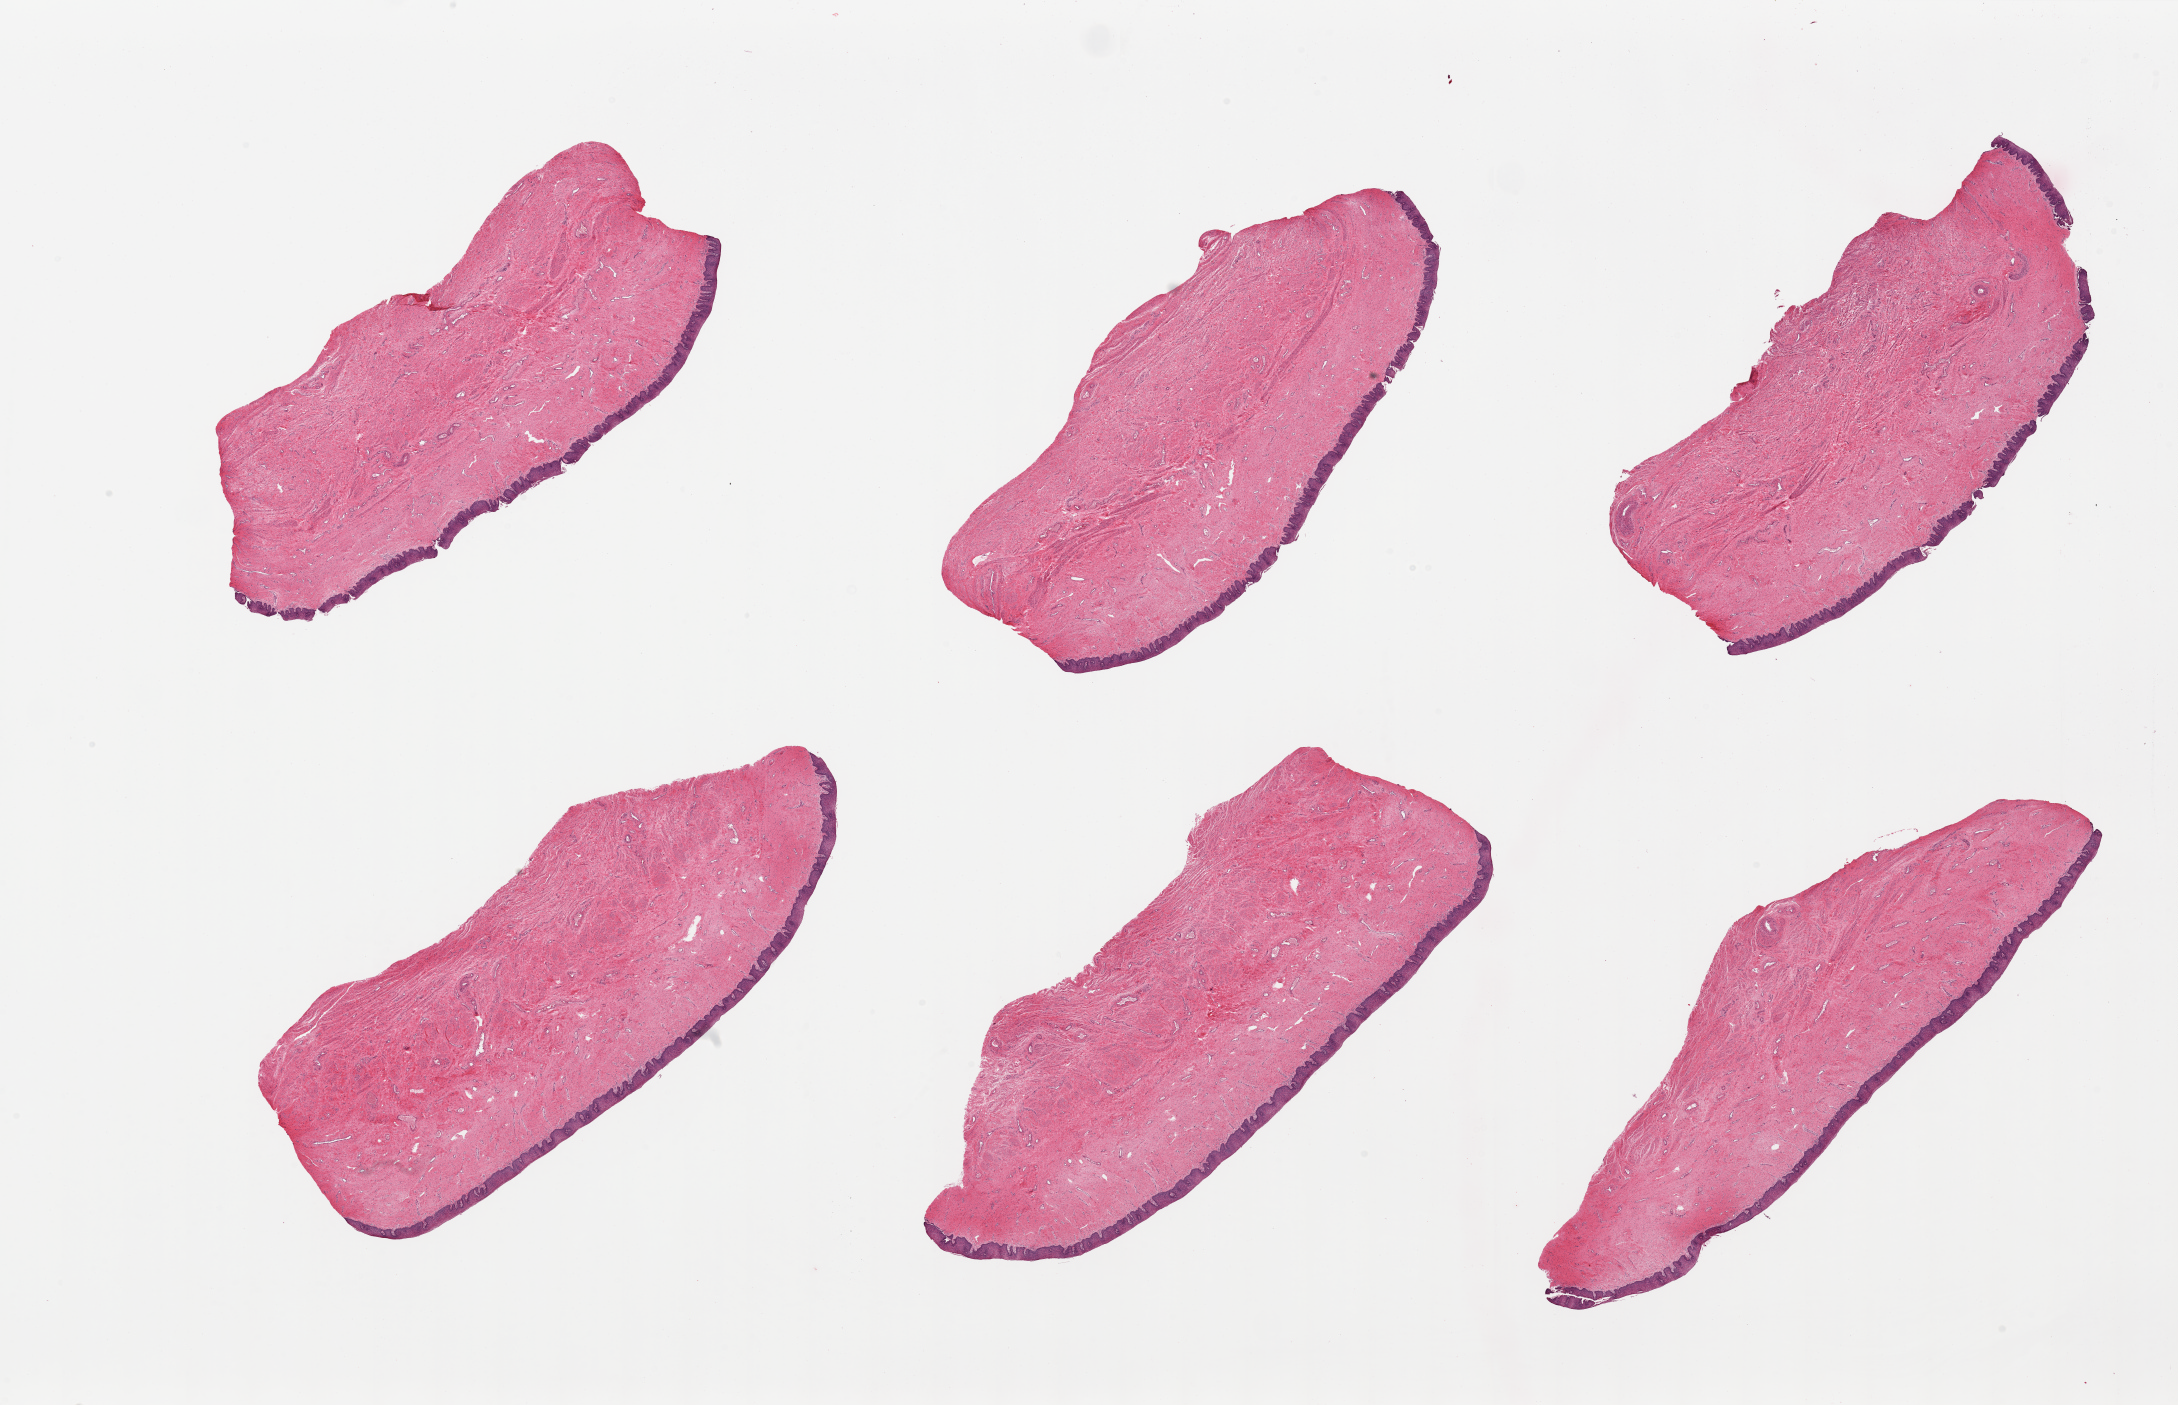
Whole-slide image, H&E stain, whole scanned area (about 34.5 x 22.2 mm, from a 20x scan) shown as a low-resolution overview; PAXgene-fixed, paraffin-embedded tissue; section of vagina (target tissue); donor tissue sample. Donor: female.
Review note (as recorded): 6 pieces, well preserved; squamous mucosa is ~5% thickness, ~0.25mm.